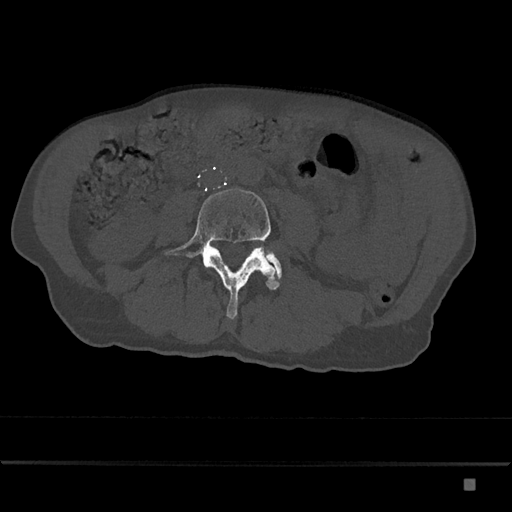
CT including the spine, one axial slice. Slice 336 of 797 in the series (ordered by position). Reconstruction kernel Br40s/3. 120 kVp. Bone window (W 1800 / L 400 HU). 0.5 mm slice thickness. 512 × 512 image matrix, field of view 390 × 390 mm. Male patient, age 72 years. From the clinical record (not read from this slice): primary cancer: prostate.
Structures marked on this image (semi-automatic segmentation, software-assisted and operator-edited):
- L4 vertebra: bounding box [x1, y1, x2, y2] px = [165, 189, 282, 319]
- L5 vertebra: [267, 254, 282, 273]